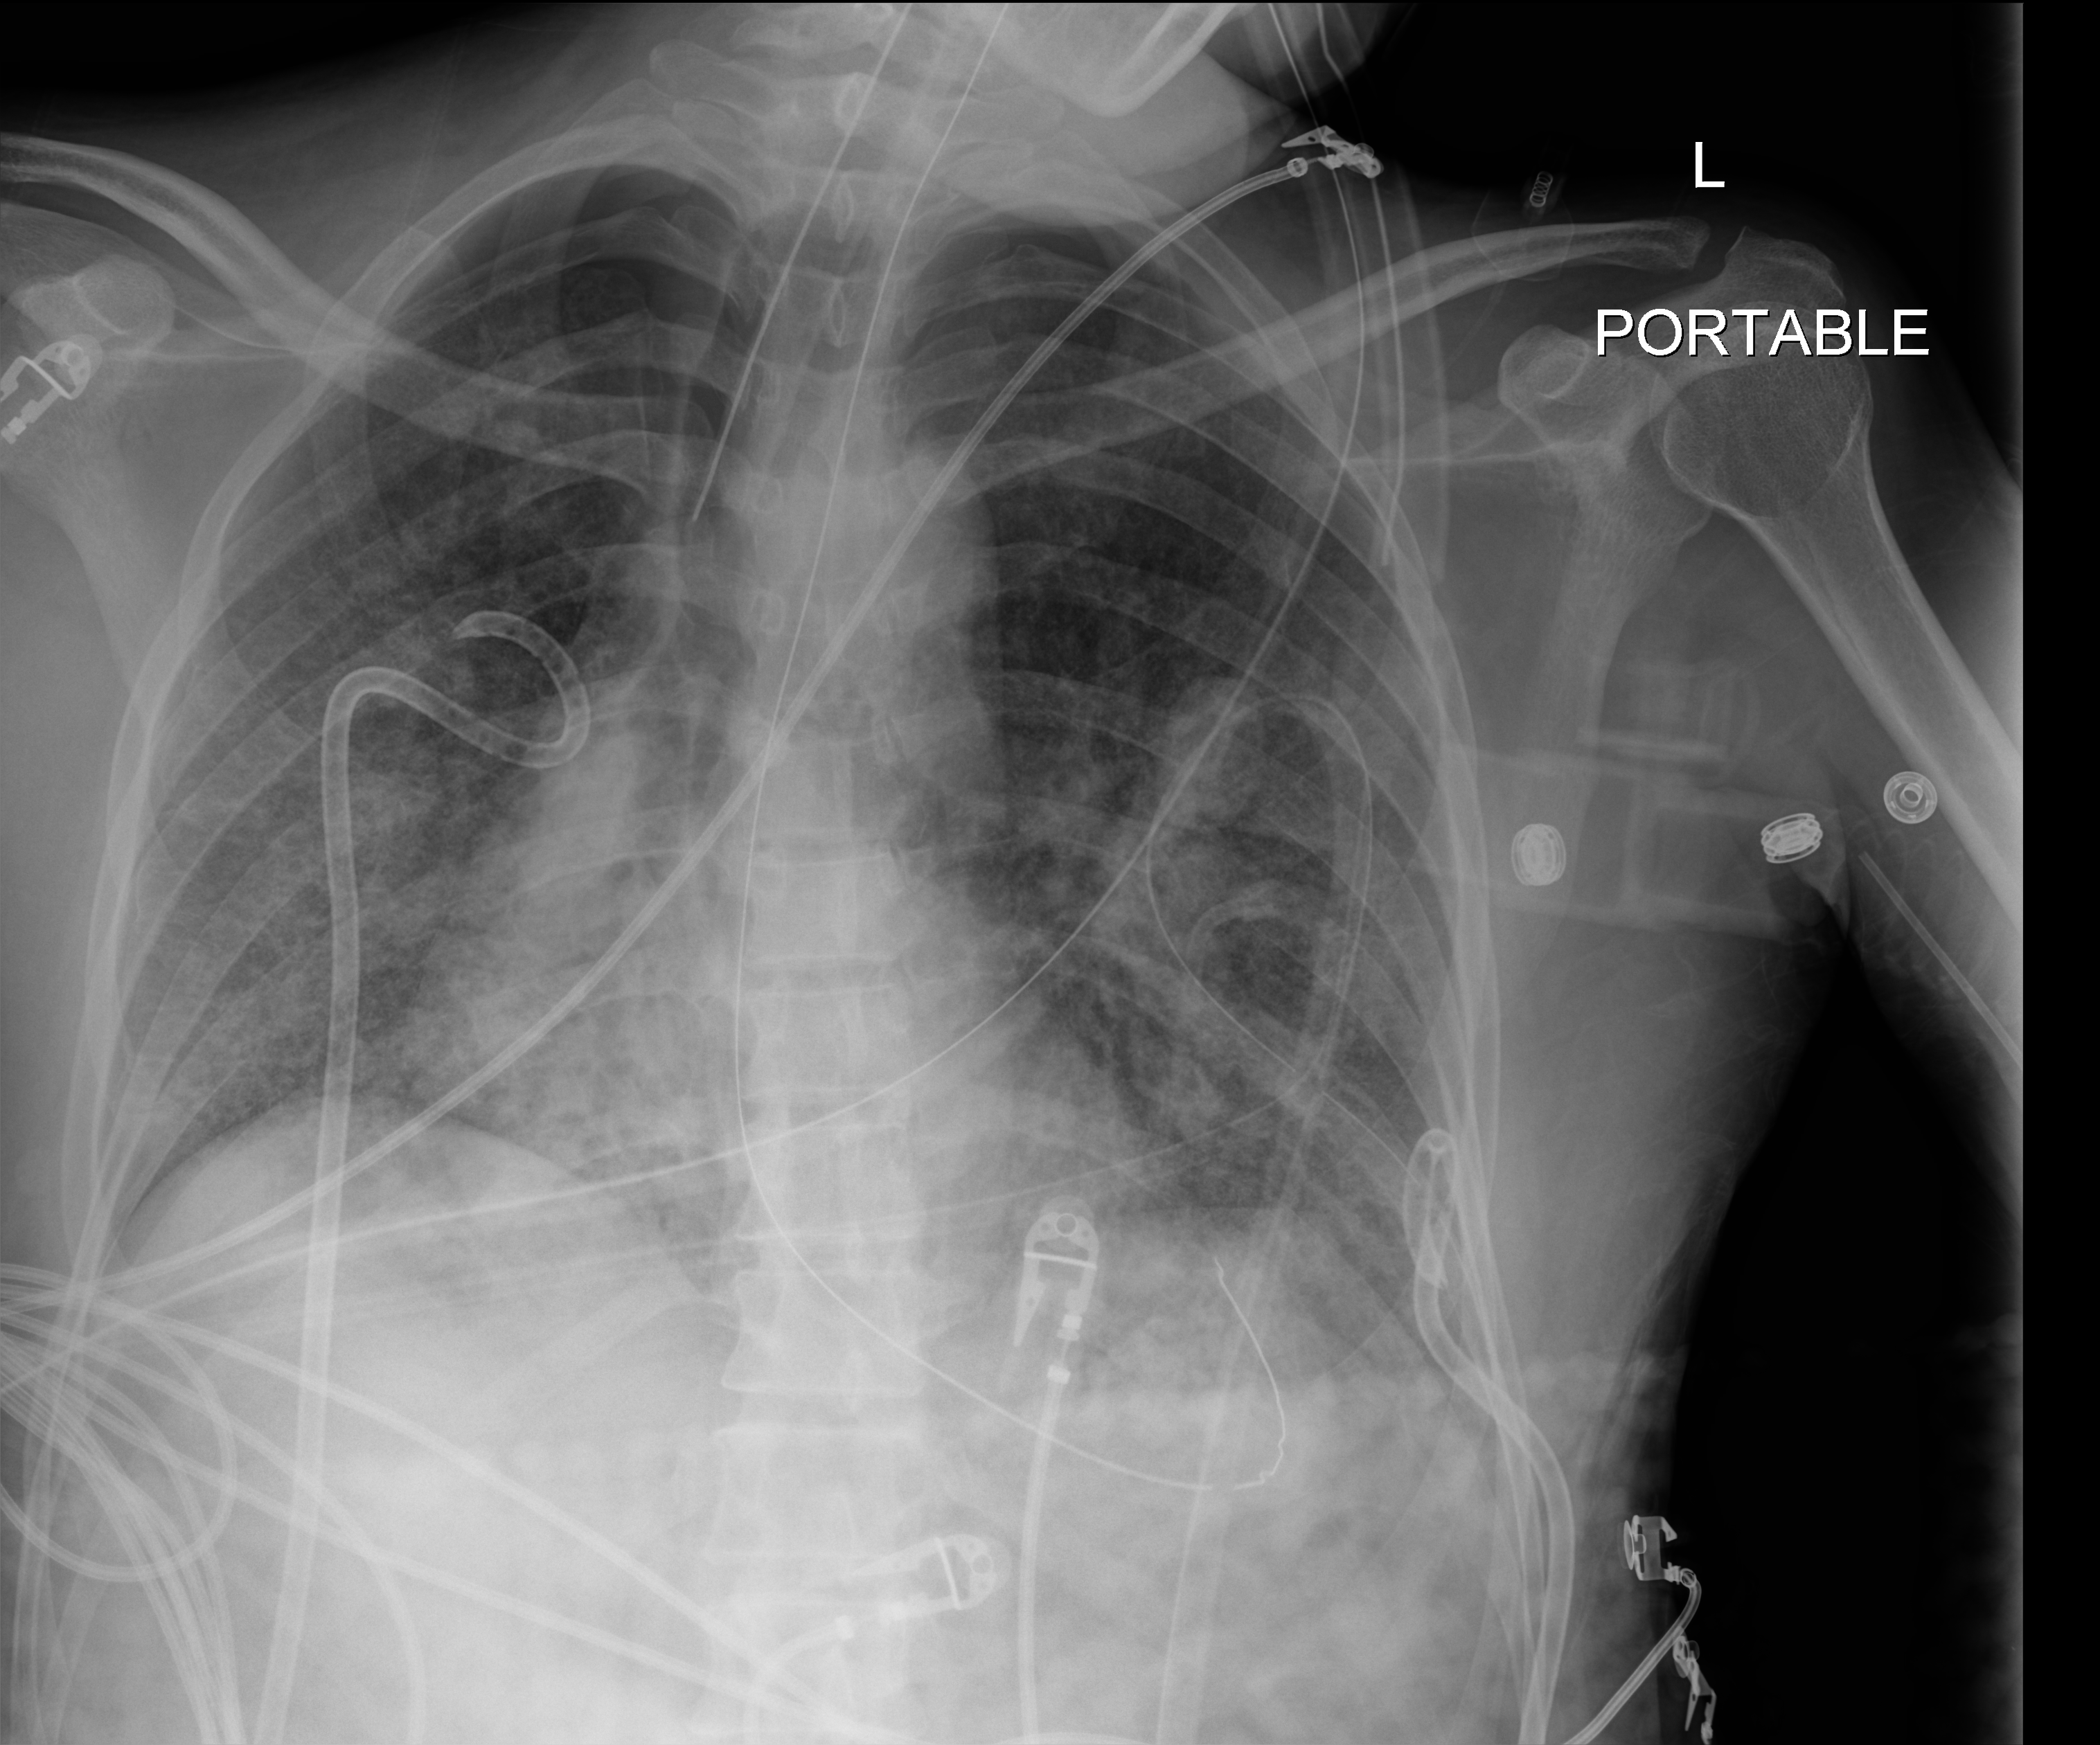
Chest radiograph (digital radiography); anteroposterior (AP) projection. Adult patient hospitalised with COVID-19, age 18–59 years.
Hospital-stay facts (about this admission, not read from this image; timing relative to this image not recorded):
- other chronic lung disease (admission record): no